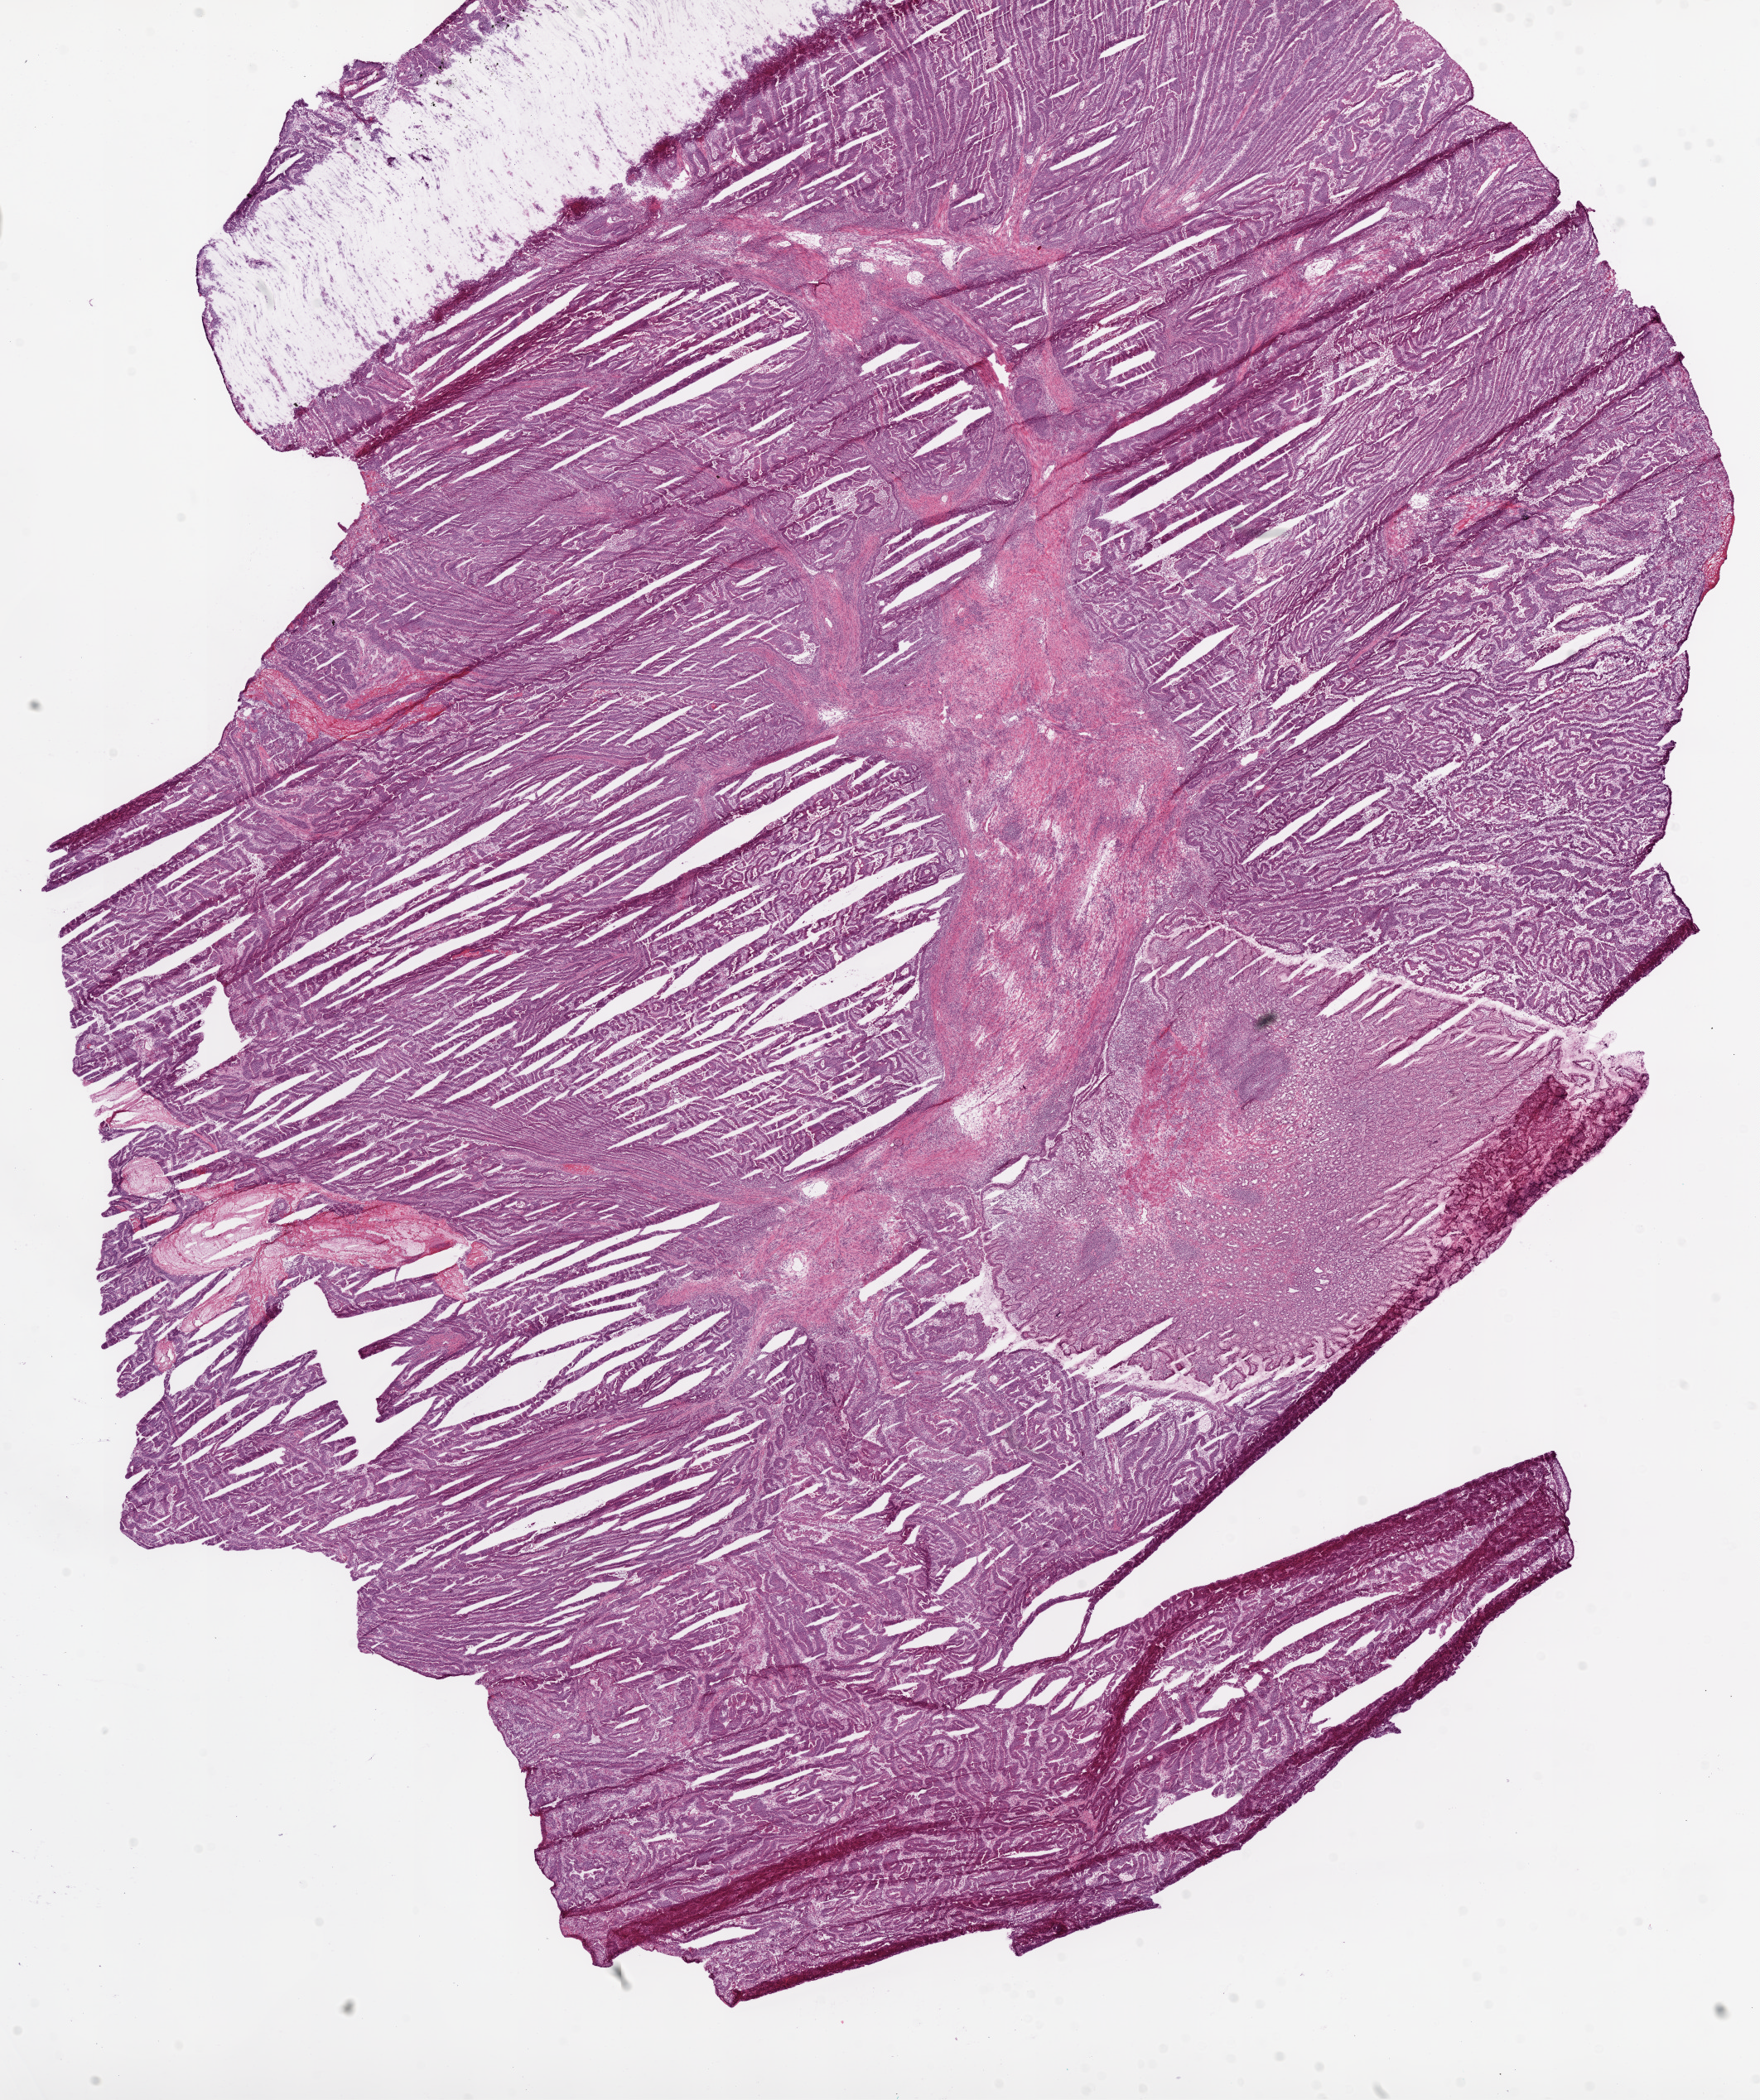
Whole-slide histology image, Hematoxylin and eosin (H&E) stained — shown as a low-resolution overview of the whole scanned area (about 17.1 x 20.3 mm, slide scanned at 20x), frozen section from the bottom of the tissue portion, primary tumour sample from the stomach. Patient: female, age at initial diagnosis 73 years. Composition of this section per pathologist review: tumour cells 75%, tumour nuclei 85%.
Diagnosis: Adenocarcinoma, NOS (body of stomach).